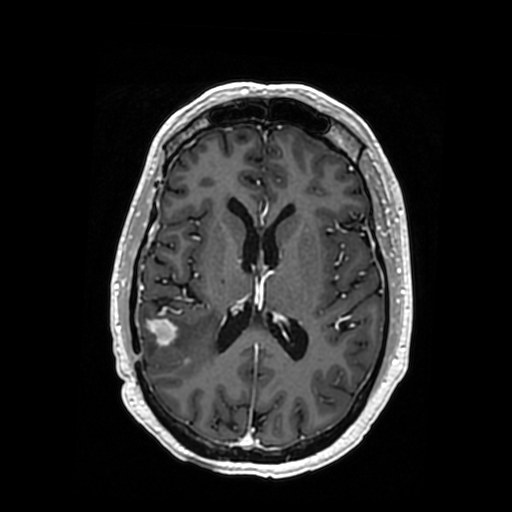
Brain MRI from a brain-tumour surgery series, one axial slice. Slice 166 of 364 in the series (ordered by position). T1-weighted post-contrast. 512 × 512 image matrix. From the clinical record (not read from this slice): histopathology: Oligodendroglioma; WHO grade: 3; IDH mutation: yes; tumour location: Right Posterior Temporal Inferior Parietal.
Structures marked on this image (expert manual segmentation):
- tumour: bounding box (x1, y1, x2, y2) in pixels: (172, 318, 214, 362)